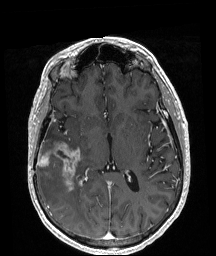
Brain MRI from a brain-tumour surgery series, one axial slice. Position 103 of 208 along the scan axis. T1-weighted post-contrast. 1 mm slice thickness. 216 × 256 image matrix. From the clinical record (not read from this slice): histopathology: Astrocytoma; WHO grade: 4; IDH mutation: yes; tumour location: Right Temporal.
Structures marked on this image (manually delineated by an expert):
- tumour: bounding box [x1, y1, x2, y2] px = [38, 143, 81, 191]